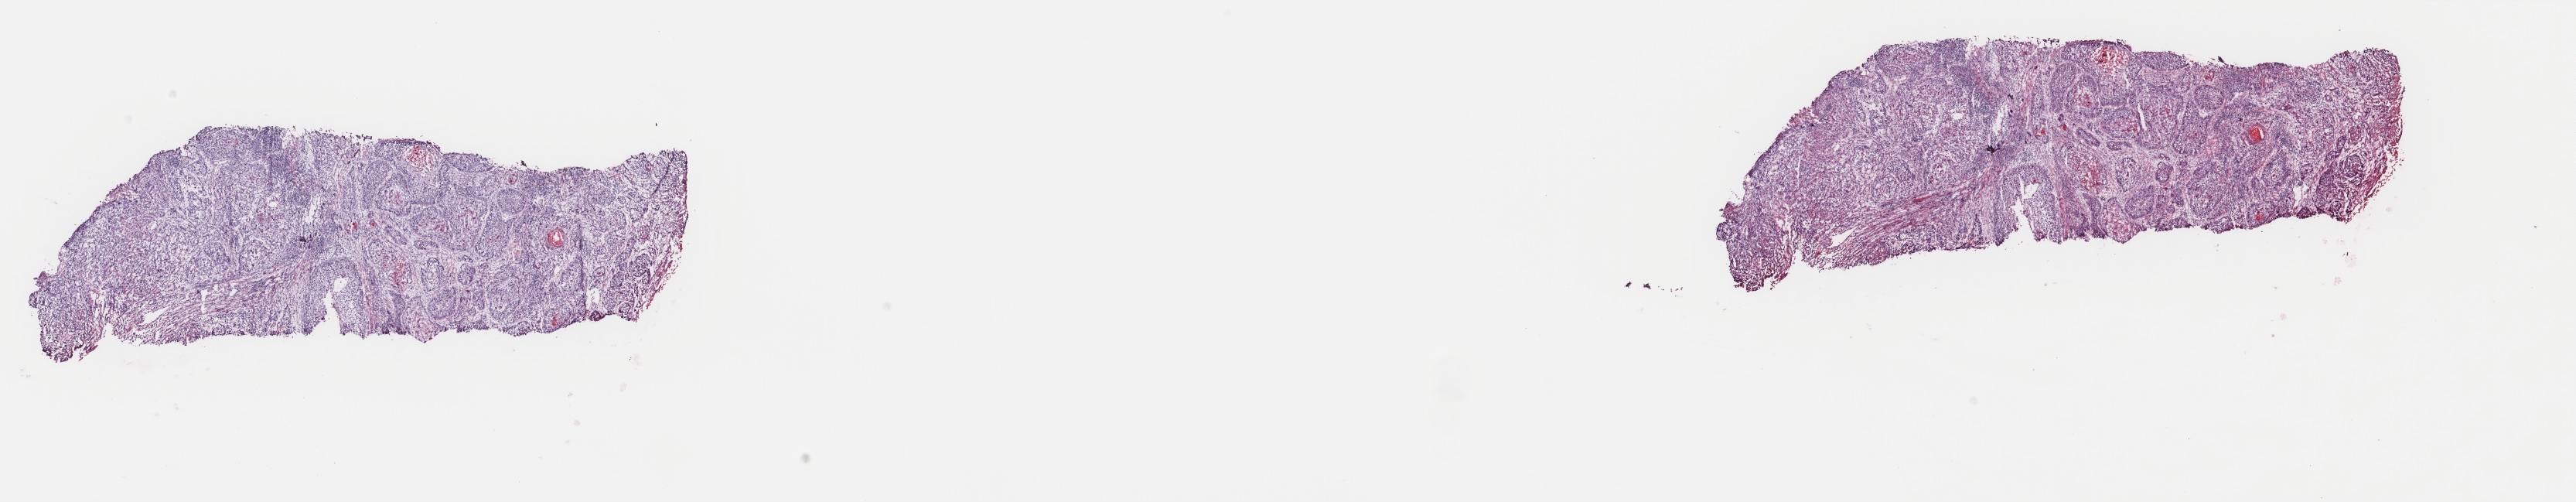
Digitized H&E-stained tissue section (whole slide), whole scanned area (about 26.4 x 5.2 mm) shown as a low-resolution overview; frozen section from the top of the tissue portion; head and neck, primary tumour sample. Patient: male, age at initial diagnosis 50 years. Histologic grade: G2 (moderately differentiated). Slide review estimates, as recorded: tumour cells 80%, tumour nuclei 90%, normal cells 0%, stromal cells 20%, necrosis 0%. Inflammatory infiltration, as recorded: lymphocyte infiltration 0%, monocyte infiltration 0%, neutrophil infiltration 0%.
- pathologic diagnosis: Squamous cell carcinoma, NOS (gum, NOS)
- lymph nodes positive (case pathology): 0 of 11 examined
- AJCC pathologic stage: IVA (7th edition)